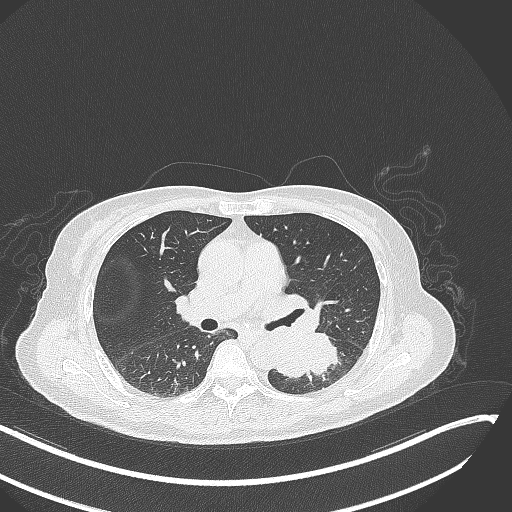
Chest CT, one axial slice. Slice 158 of 342 in the series (ordered by position). Reconstruction kernel B70f. Lung window (W 1500 / L -600 HU). 512 × 512 image matrix, field of view 400 × 400 mm. Female patient, age 64 years. Case-level facts recorded for this patient, not image findings: clinical TNM (as recorded): T3 N1 M1; histopathological grade: G3.
Structures marked on this image (bounding box drawn by a radiologist):
- lung tumour (recorded histology: small cell carcinoma): bounding box [x1, y1, x2, y2] px = [277, 328, 344, 383]